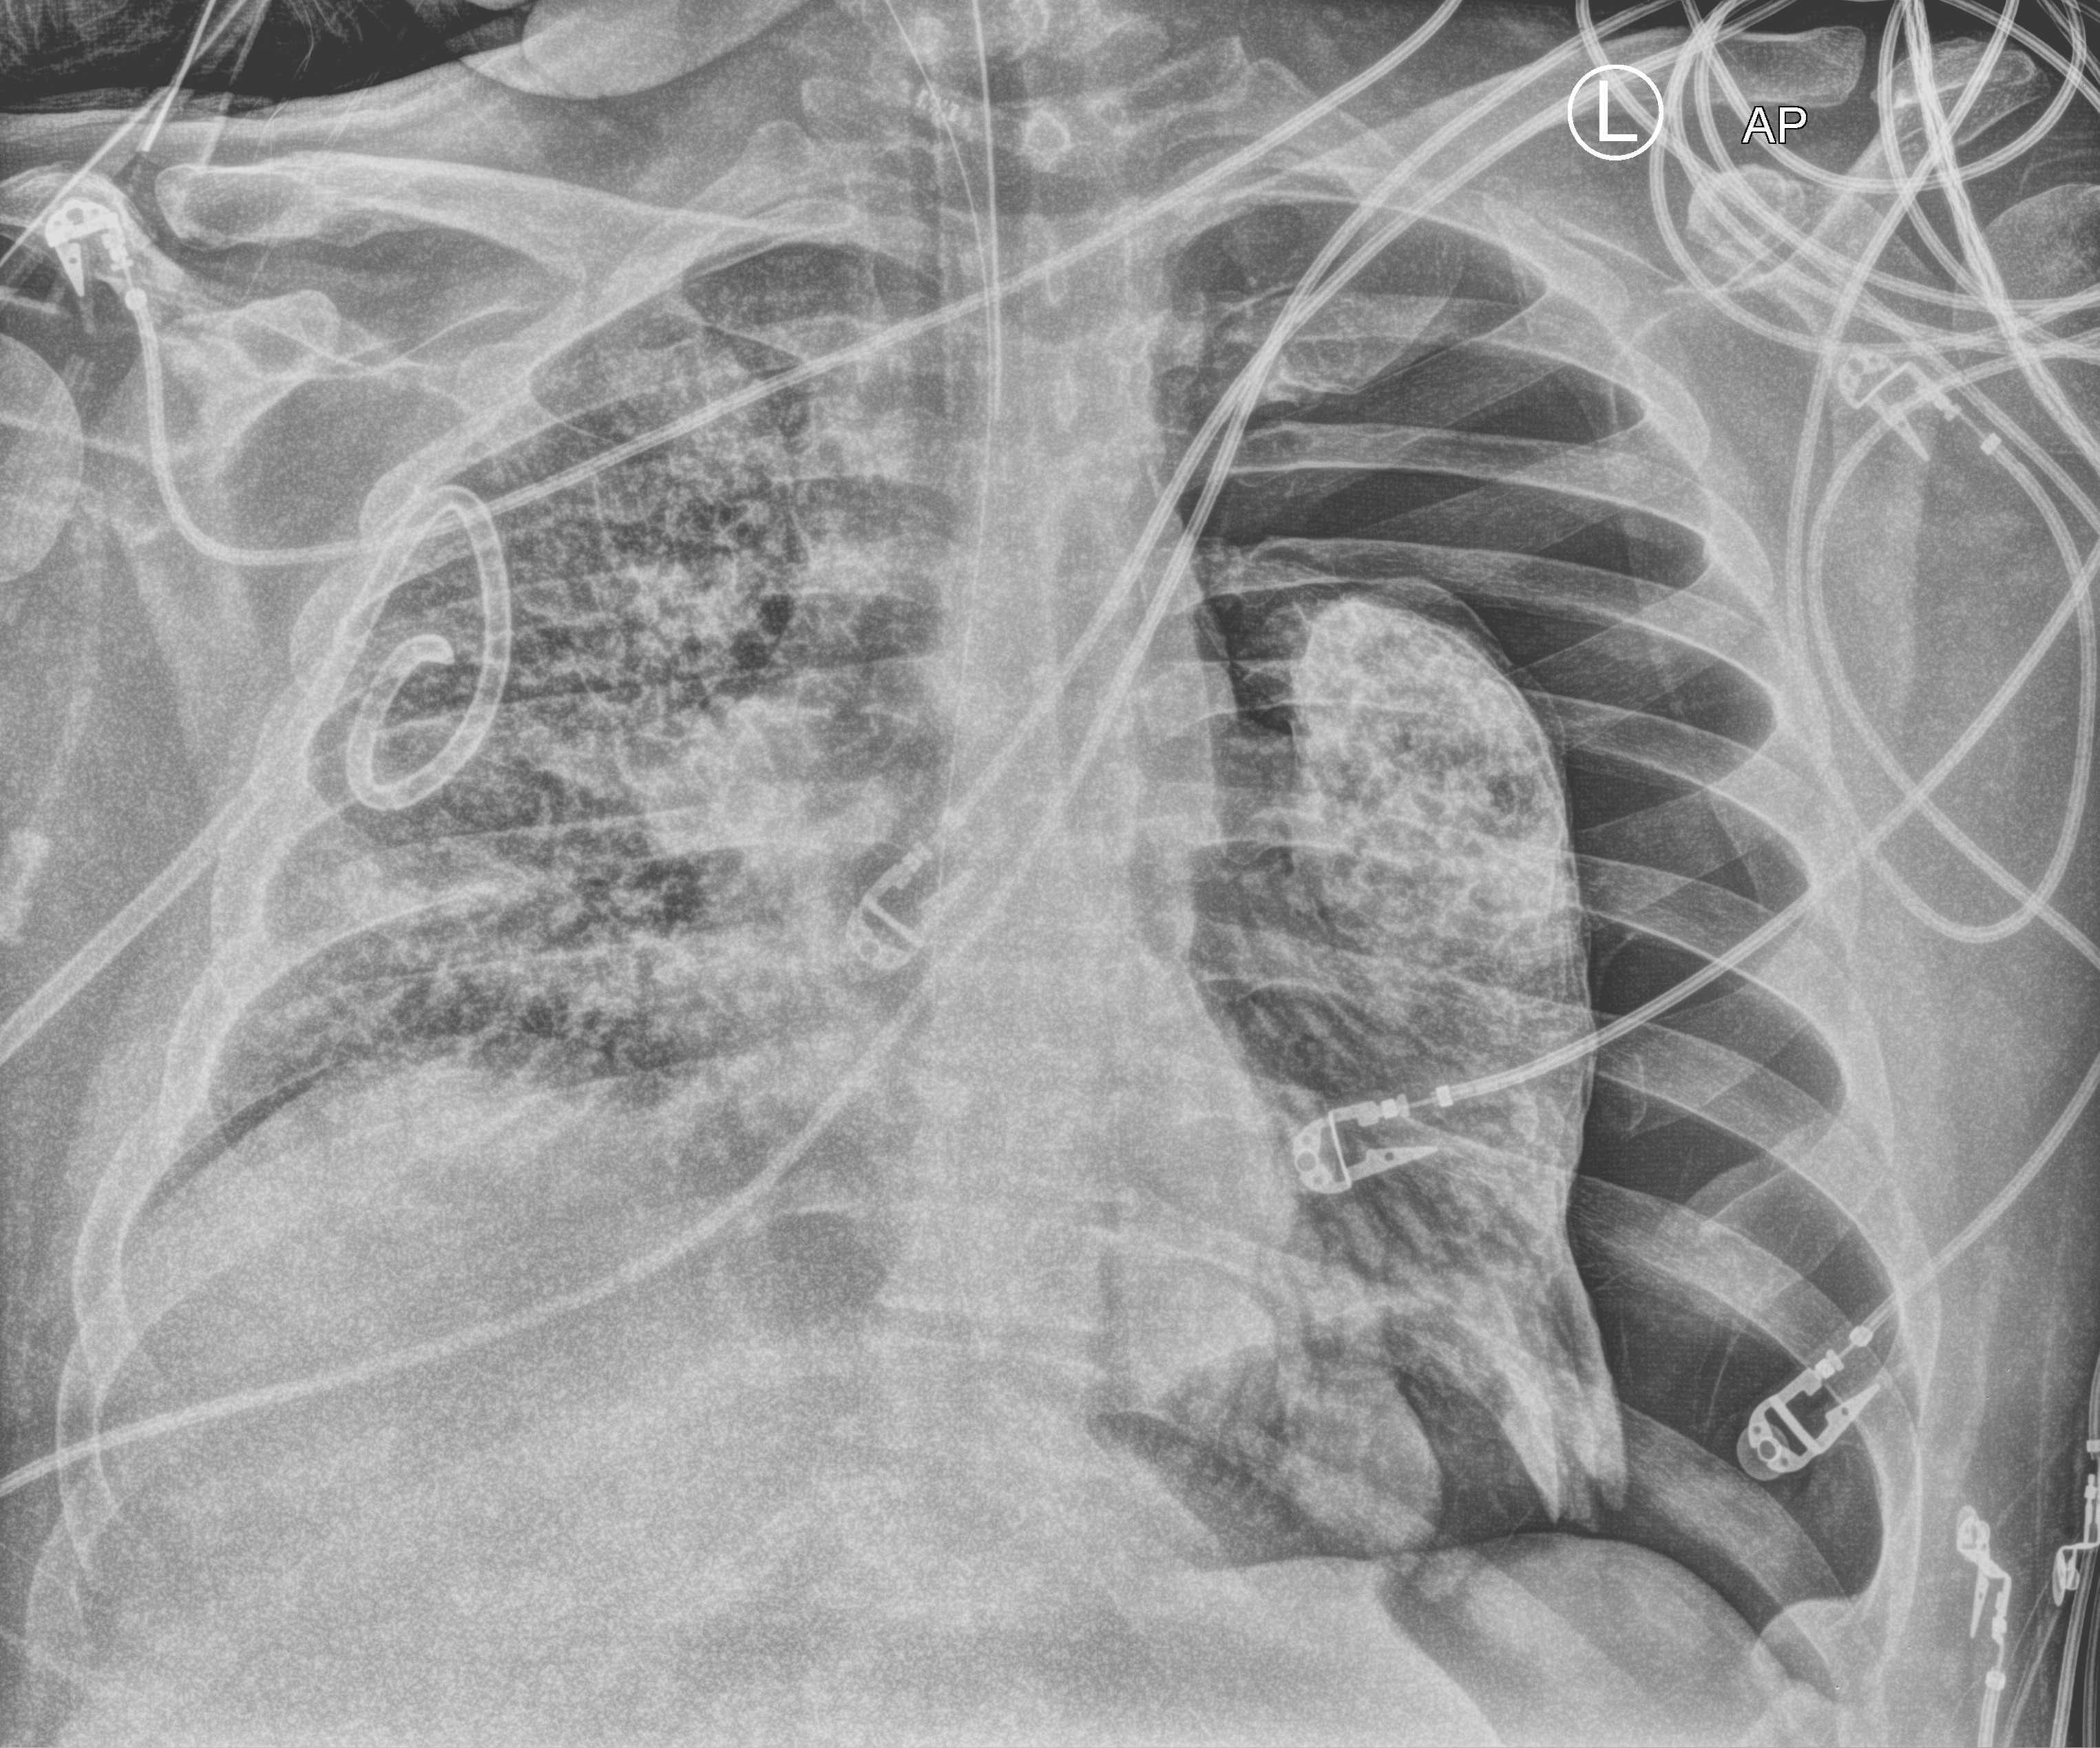
Chest X-ray (portable), anteroposterior (AP) projection. Adult patient hospitalised with COVID-19, age 18–59 years.
Hospital-stay facts (about this admission, not read from this image; timing relative to this image not recorded):
- mechanically ventilated during this hospital stay: yes